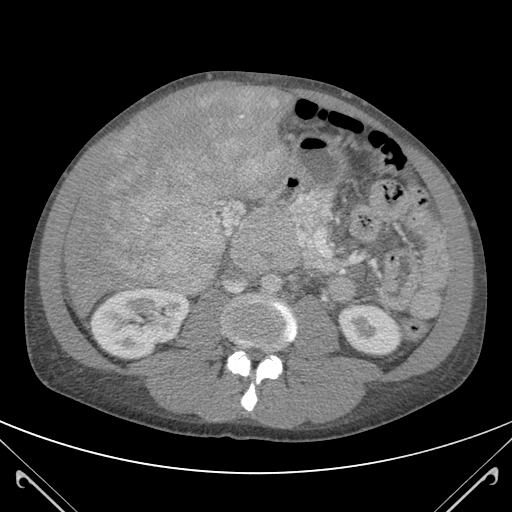
Contrast-enhanced abdominal CT (liver protocol), one axial slice; slice 44 of 118 in the series (ordered by position); soft-tissue window (W 400 / L 40 HU); 3 mm slice thickness; 512 × 512 image matrix. From the clinical record (not read from this slice): diagnosis: hepatocellular carcinoma (patient treated with transarterial chemoembolisation; whether this scan precedes or follows treatment is not stated here); TNM stage (as recorded): Stage-IIIB; Child-Pugh class: A; tumour nodularity: uninodular.
Structures marked on this image (semi-automatically segmented with operator editing):
- abdominal aorta: box from (x=262, y=274) to (x=281, y=296) px
- liver parenchyma outside the tumour (the mass and vessels are separate outlines, so this box may not span the whole liver): (x=65, y=87)–(x=285, y=312)
- mass: (x=94, y=87)–(x=289, y=286)
- liver vessels: (x=176, y=286)–(x=178, y=288)